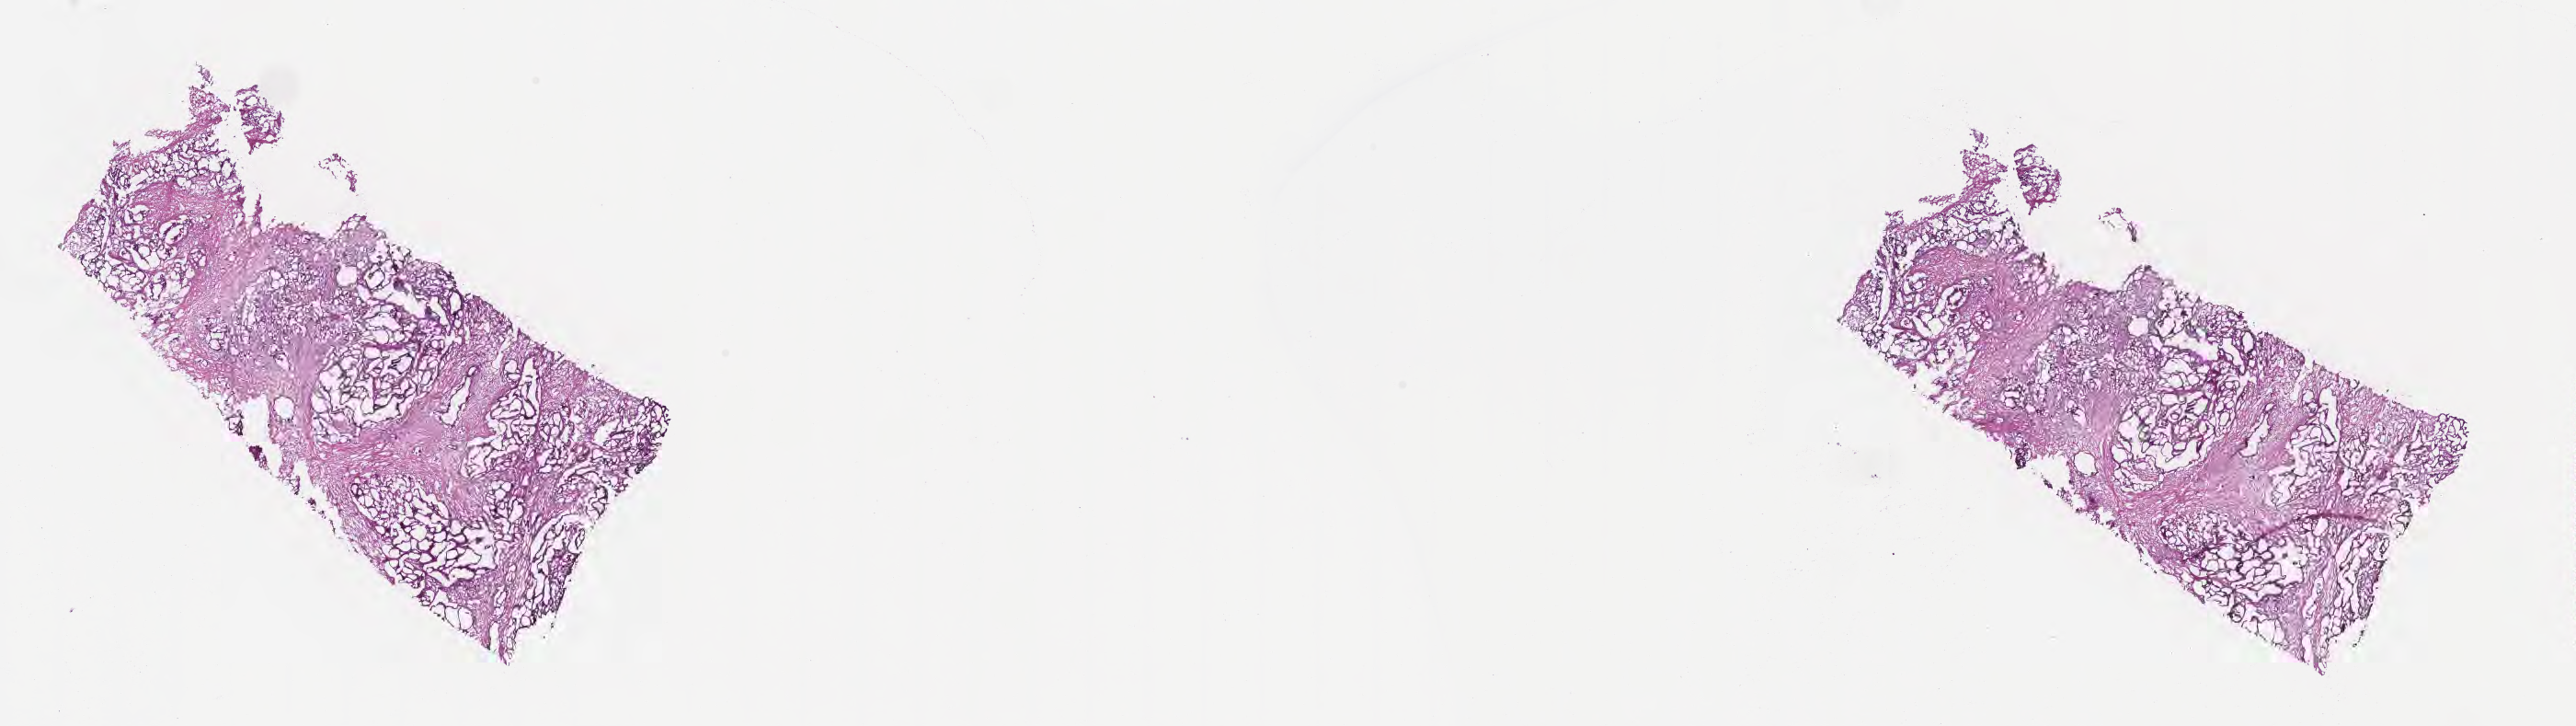
Haematoxylin and eosin whole-slide image — whole scanned area (about 22.6 x 6.4 mm) shown as a low-resolution overview; cryosection; specimen: primary tumor; site: head of pancreas. Patient: male, age at initial diagnosis 55 years. Tumor grade: G2 (moderately differentiated). Pathologist review of this section (percent, as recorded): tumor cells 54%, tumor nuclei 88%, stromal cells 45%, necrosis 1%, normal cells 0%. Infiltration values recorded for this section: lymphocyte infiltration 8%, monocyte infiltration 1%, neutrophil infiltration 0%.
Histologic diagnosis: Infiltrating duct carcinoma, NOS. Section: bottom of the tissue portion. AJCC pathologic stage: Stage III.